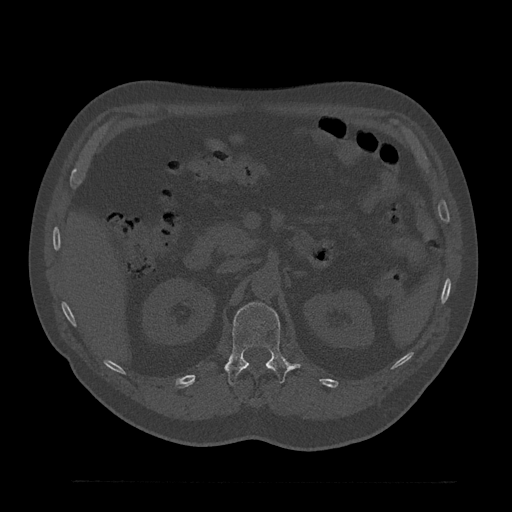
CT including the spine, one axial slice; slice 179 of 797 in the series (ordered by position); 120 kVp; bone window (W 1800 / L 400 HU); 0.5 mm slice thickness; 512 × 512 image matrix. Patient: male, 61 years. From the clinical record (not read from this slice): primary cancer: prostate.
Annotated regions visible in this slice (semi-automatic segmentation, software-assisted and operator-edited):
- L1 vertebra: bounding box [x1, y1, x2, y2] px = [225, 302, 299, 386]